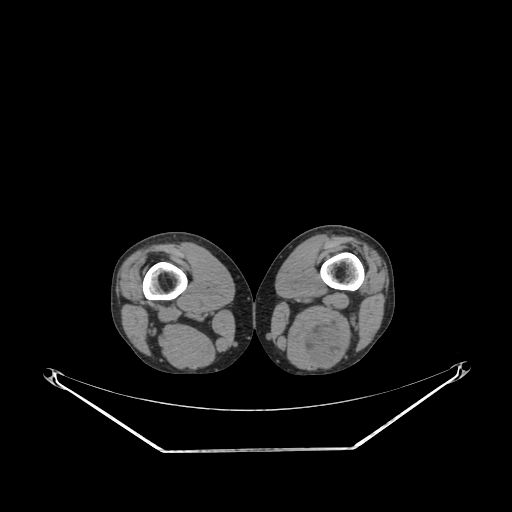
CT of an extremity soft-tissue mass (from a PET/CT study), one axial slice; position 199 of 267 along the scan axis; reconstruction kernel SOFT; soft-tissue window (W 400 / L 40 HU); 512 × 512 image matrix, field of view 500 × 500 mm. Male patient. From the clinical record (not read from this slice): histological type: synovial sarcoma; site of the primary tumour: left poplietal fossa.
Structures marked on this image (expert contour drawn on MRI and transferred to this co-registered scan by the dataset authors):
- gross tumour volume (mass): bounding box (x1, y1, x2, y2) in pixels: (301, 322, 341, 364)